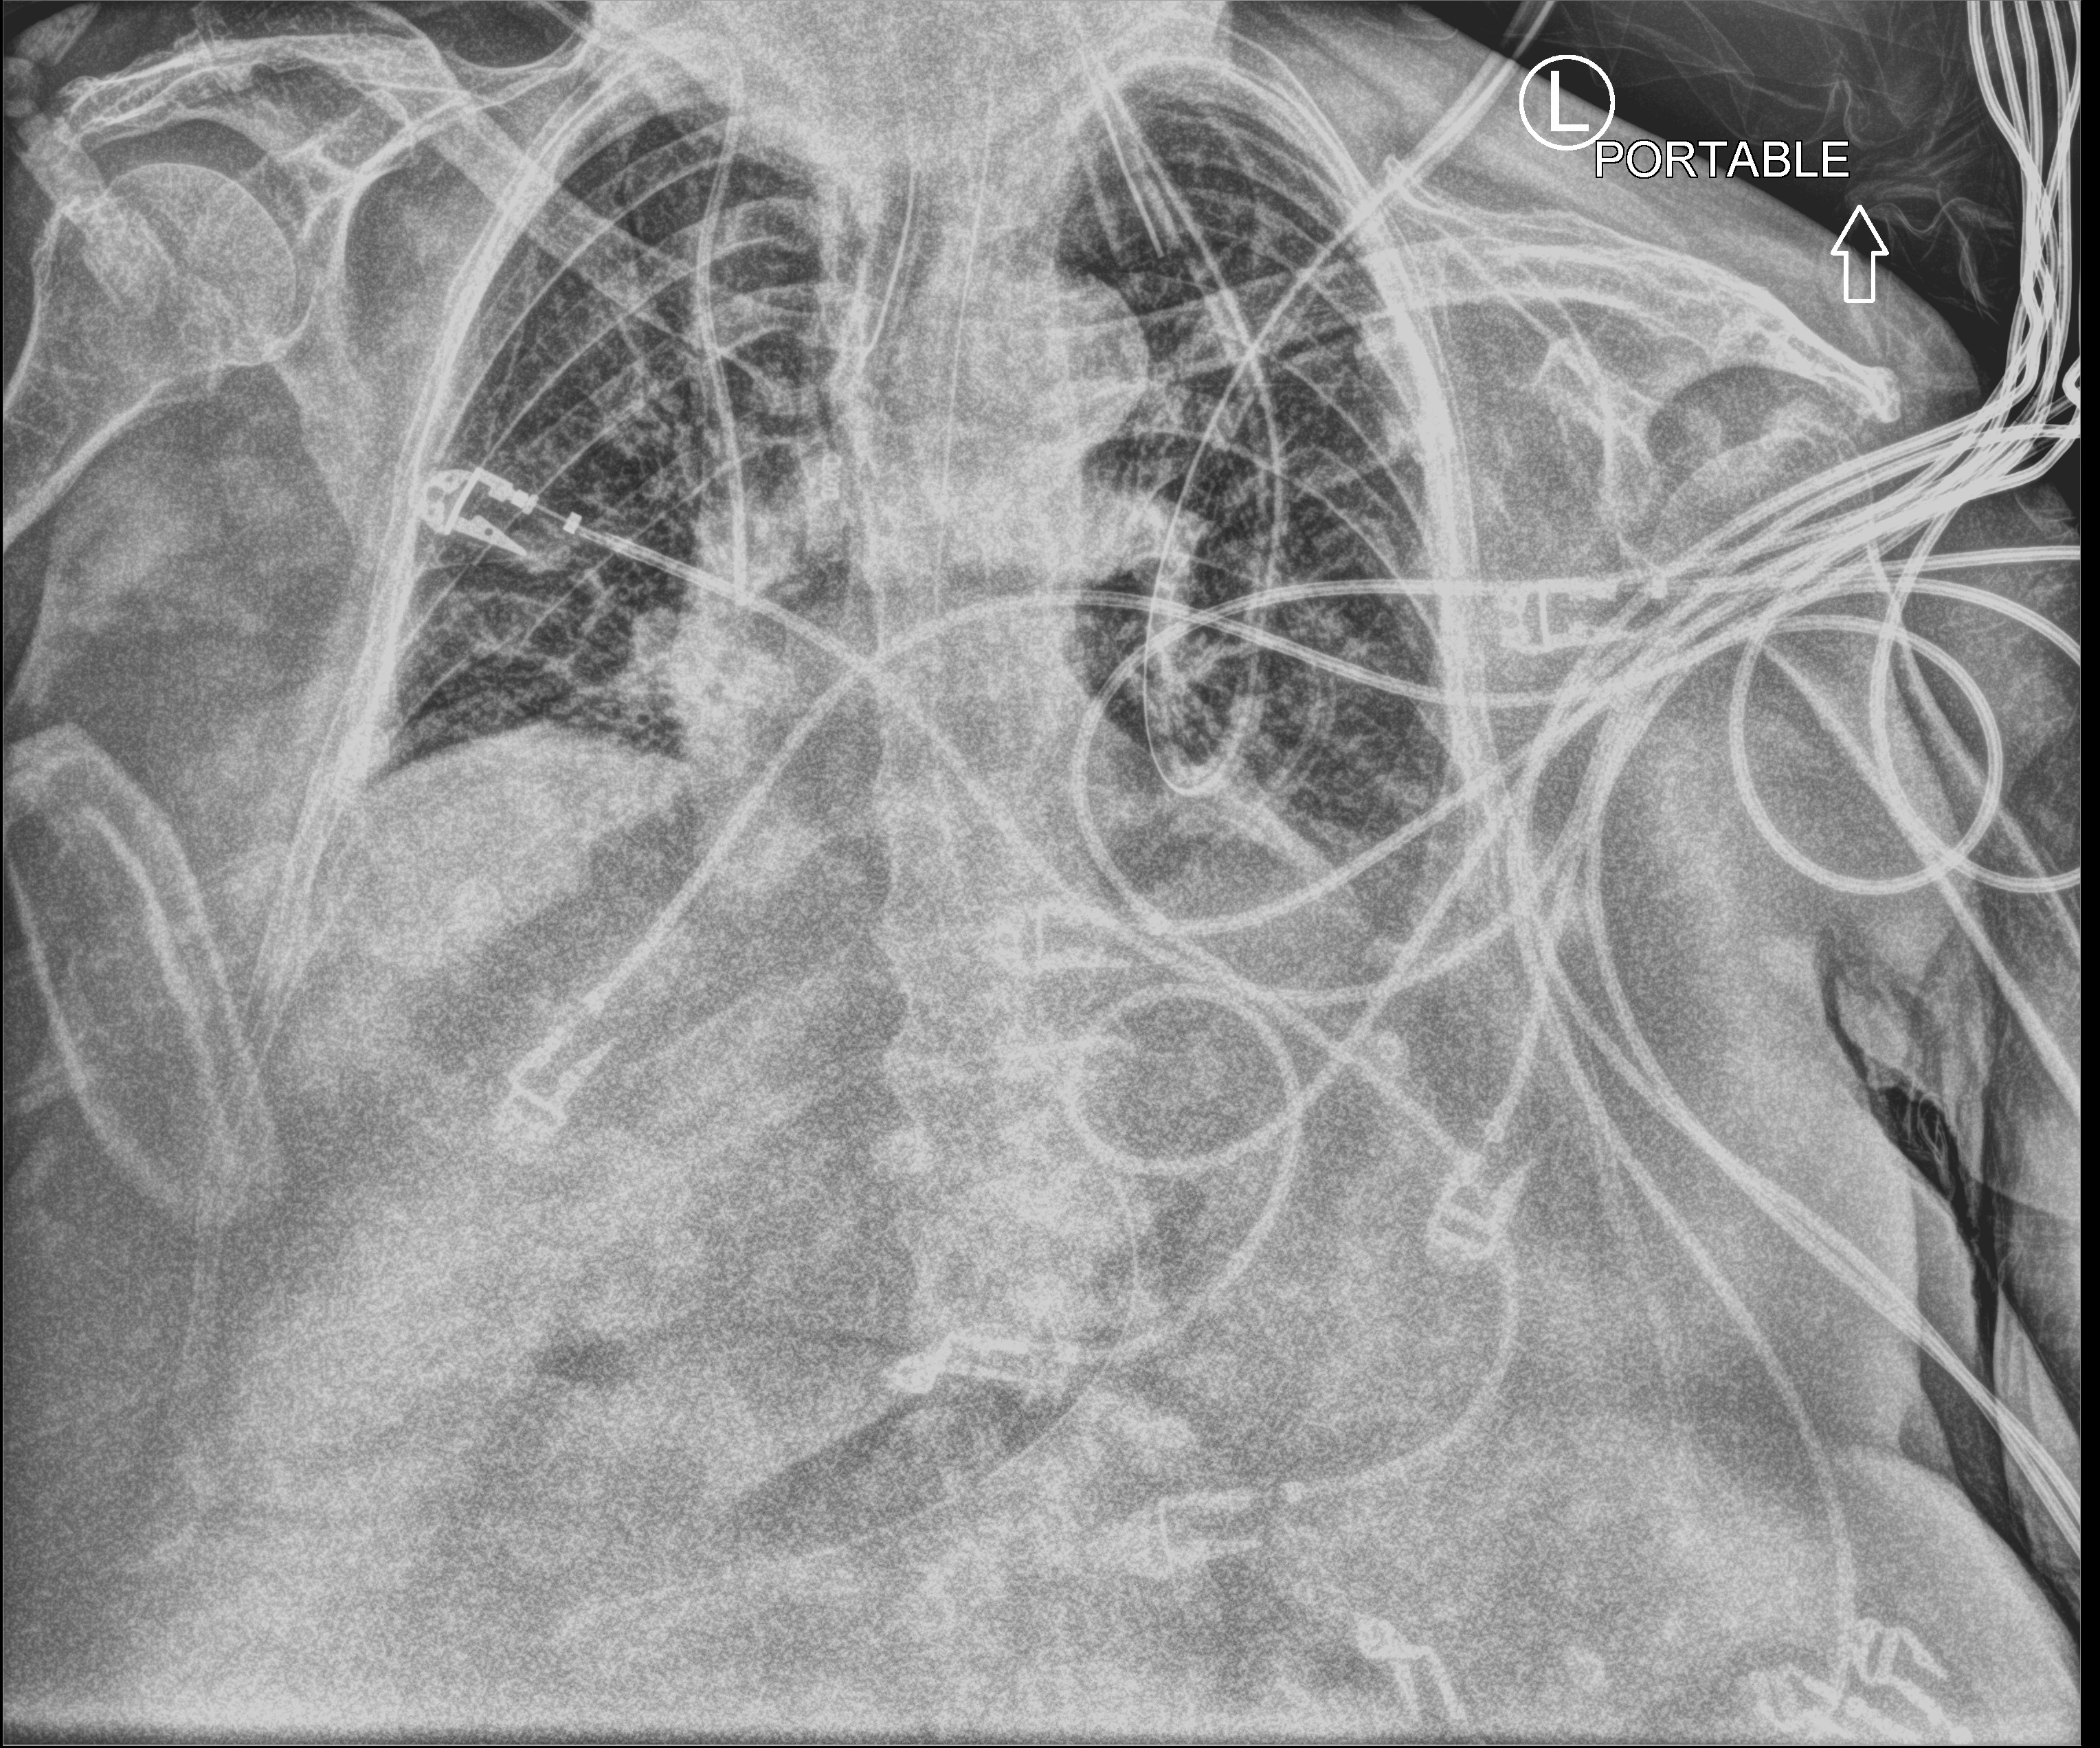
Portable chest radiograph, anteroposterior (AP) projection. Patient hospitalised with COVID-19; female, aged 75–90 years.
From the hospital-stay record, not from the radiograph (when in the stay this image was taken is not recorded): mechanically ventilated during this hospital stay: yes; smoking status (admission record): never.